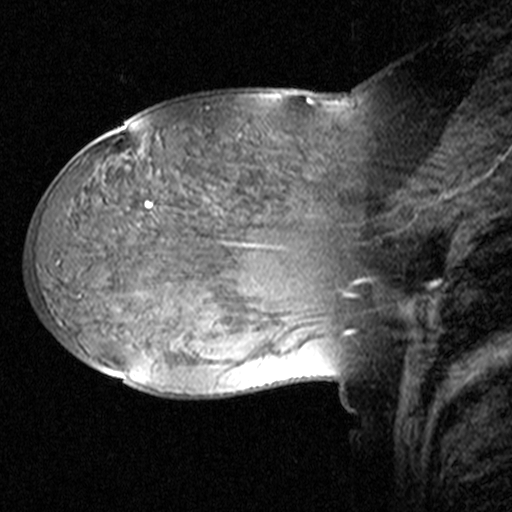
Breast MRI (dynamic contrast-enhanced), one sagittal slice. Position 26 of 44 along the scan axis. Dynamic contrast-enhanced study with each time point stored as its own series, time point 2 of 3 at this slice position (early post-contrast, ordered by acquisition time). 1.5 T. TE 4.5 ms, TR 11 ms. 3 mm slice thickness. 512 × 512 image matrix. Female patient, age 38 years. Case-level facts recorded for this patient, not image findings: setting: breast cancer imaged before/during neoadjuvant chemotherapy; receptor status: HR-positive, HER2-negative.
Outlined on this slice (semi-automatic segmentation, software-assisted and operator-edited):
- analysis volume of interest (the breast-tissue region the enhancement analysis was run in; not a lesion): bounding box (x1, y1, x2, y2) in pixels: (124, 106, 405, 245)
- tumour enhancement mask (voxels above the 90 % enhancement threshold inside the analysis volume of interest): (147, 202, 151, 207)